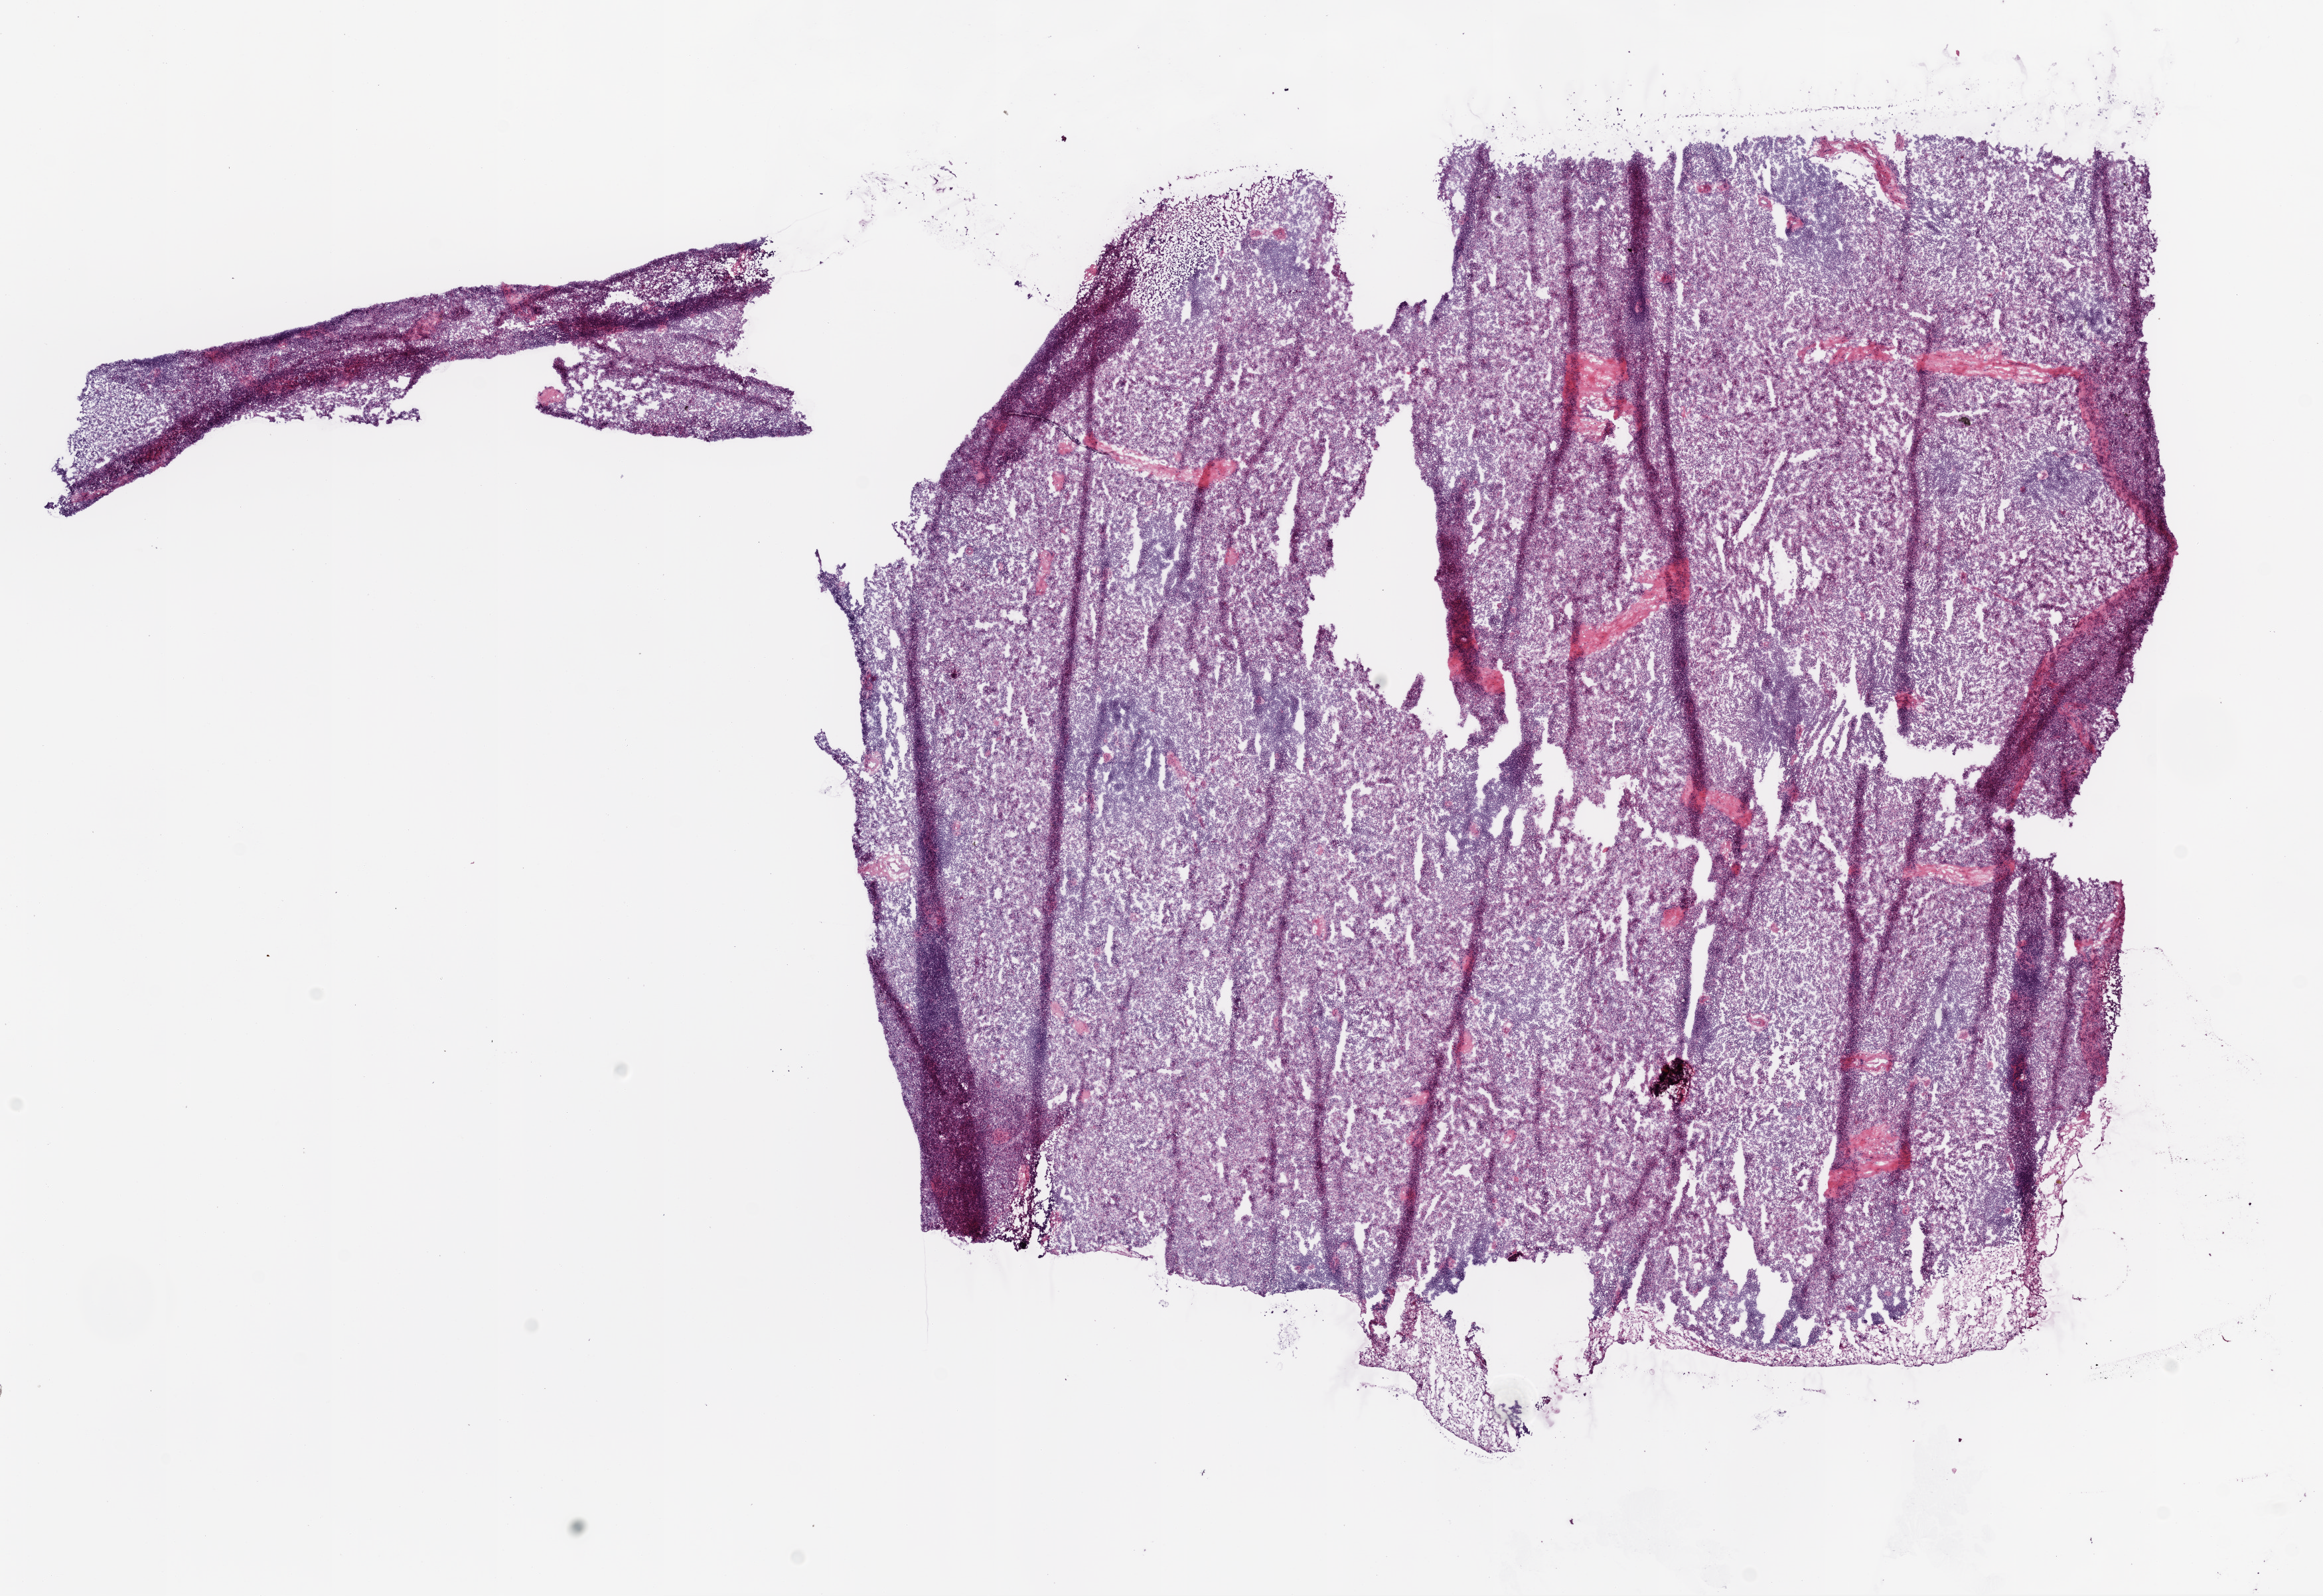
Hematoxylin and eosin (H&E) stained whole-slide image — a low-resolution overview of the entire scanned area, about 14.0 x 9.6 mm (acquisition: 20x scan). Frozen section from the bottom of the tissue portion. Ovary, solid tissue normal (non-tumour tissue) sample. Female, age 59 years at initial diagnosis.
* this section: solid tissue normal sample (biorepository sample class)
* patient diagnosis: Serous cystadenocarcinoma, NOS